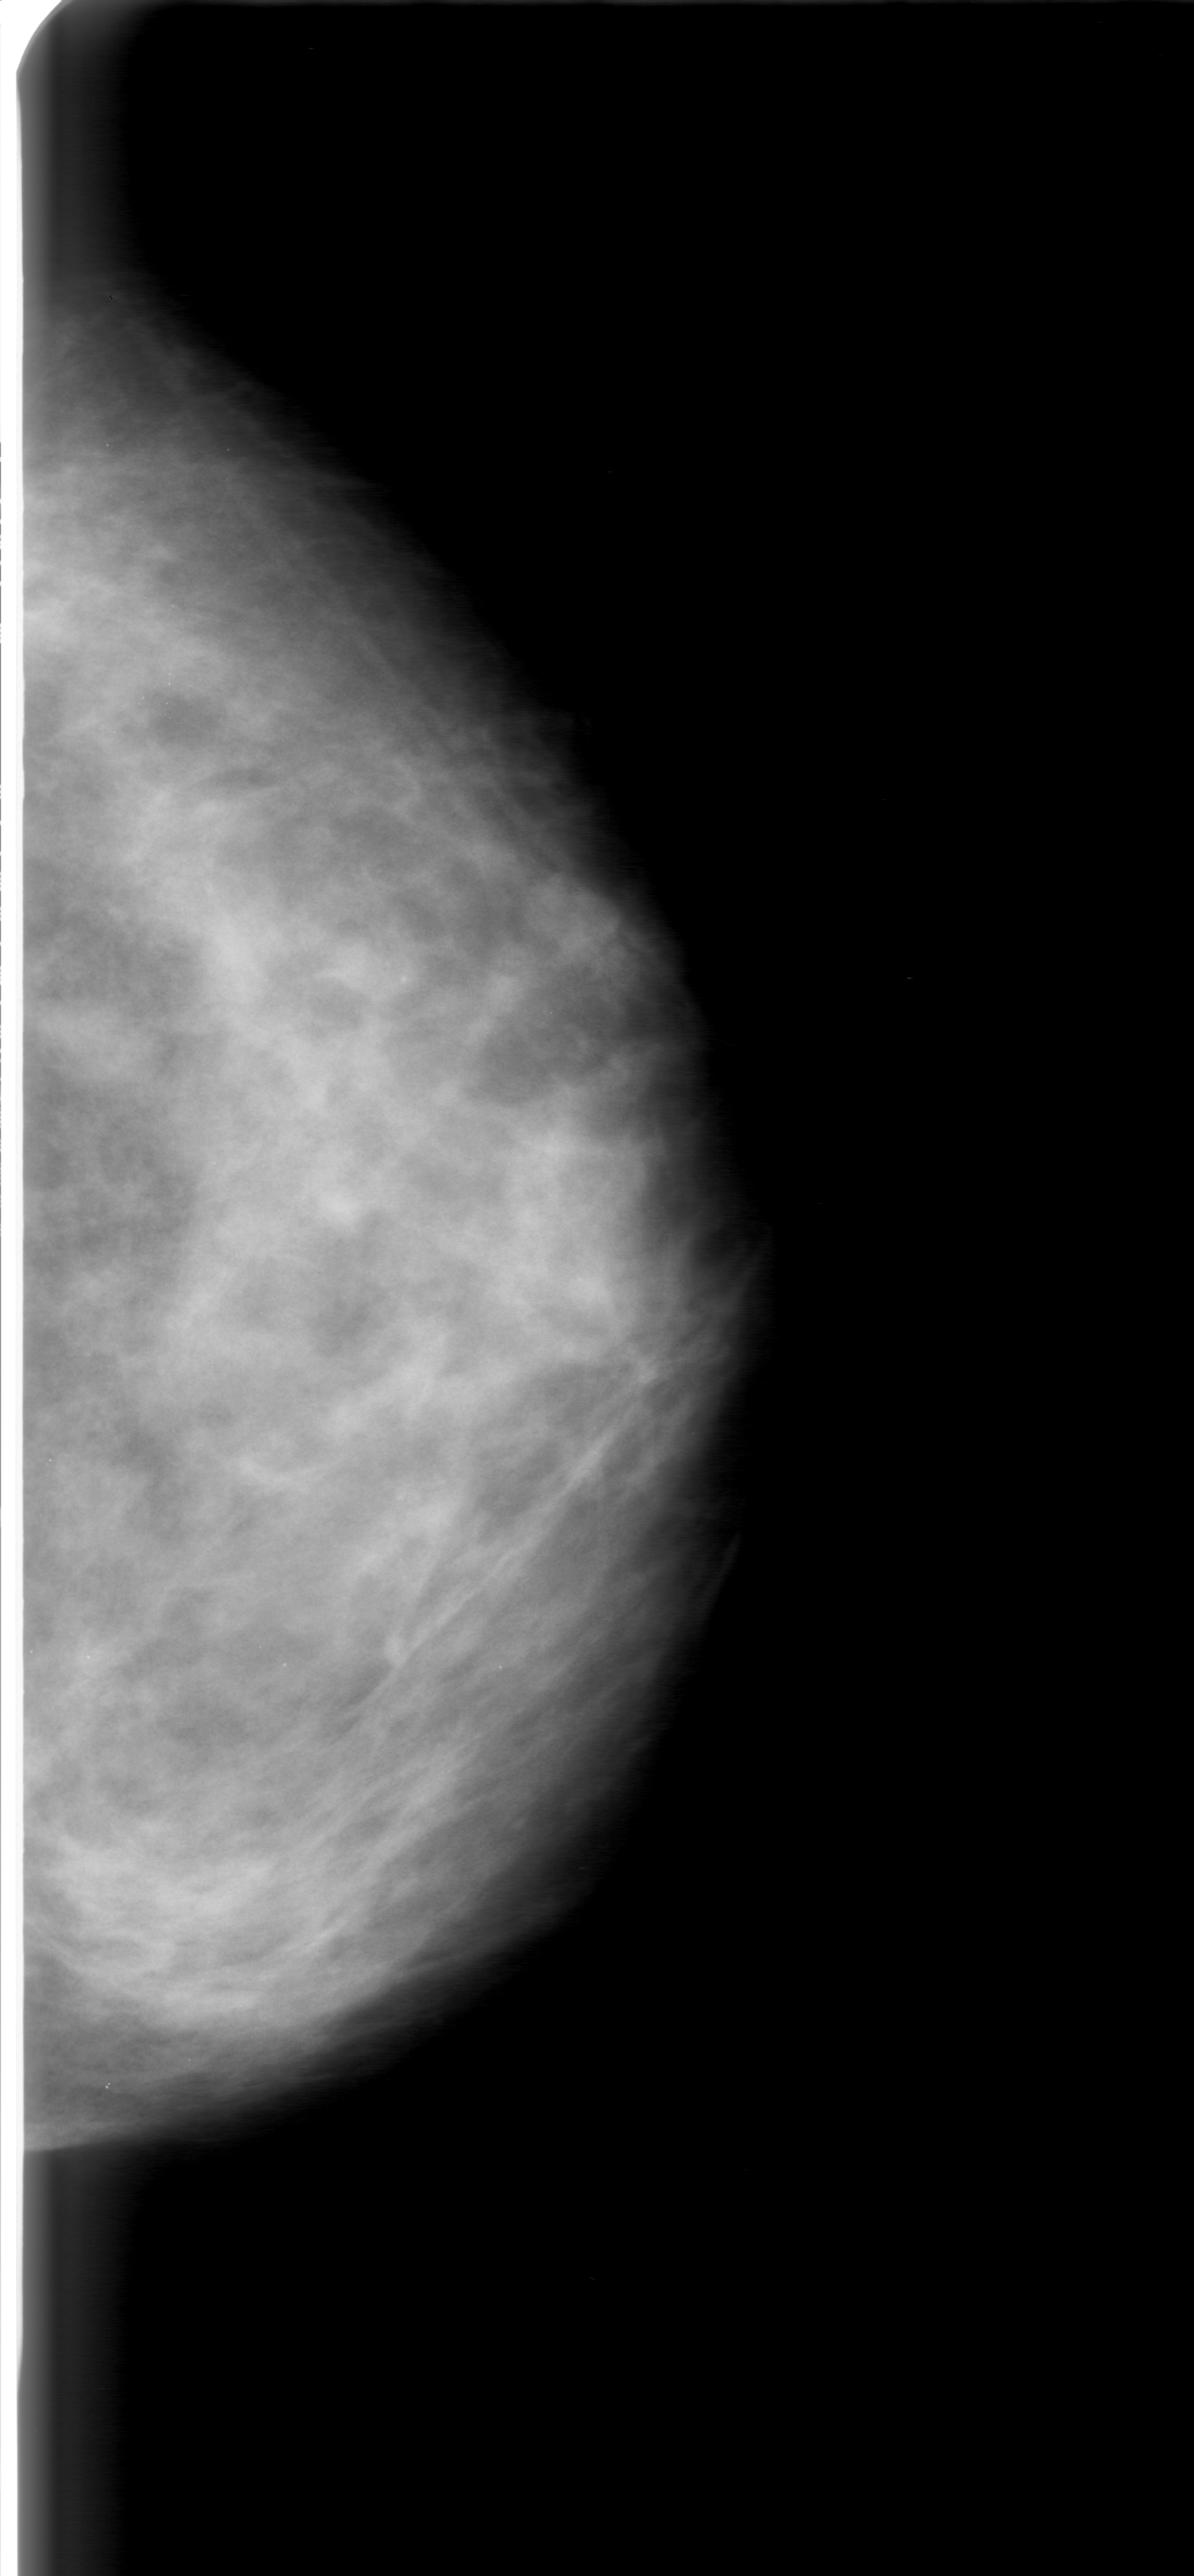
Scanned film-screen mammogram, left breast, CC view.
Marked findings (only marked abnormalities are described; nothing is implied about the rest of the image): mass, shape lobulated, margins microlobulated; BI-RADS assessment category 0 (incomplete: needs additional imaging); subtlety rating 3 on a 1 (subtle) to 5 (obvious) scale; pathology (as recorded): benign.